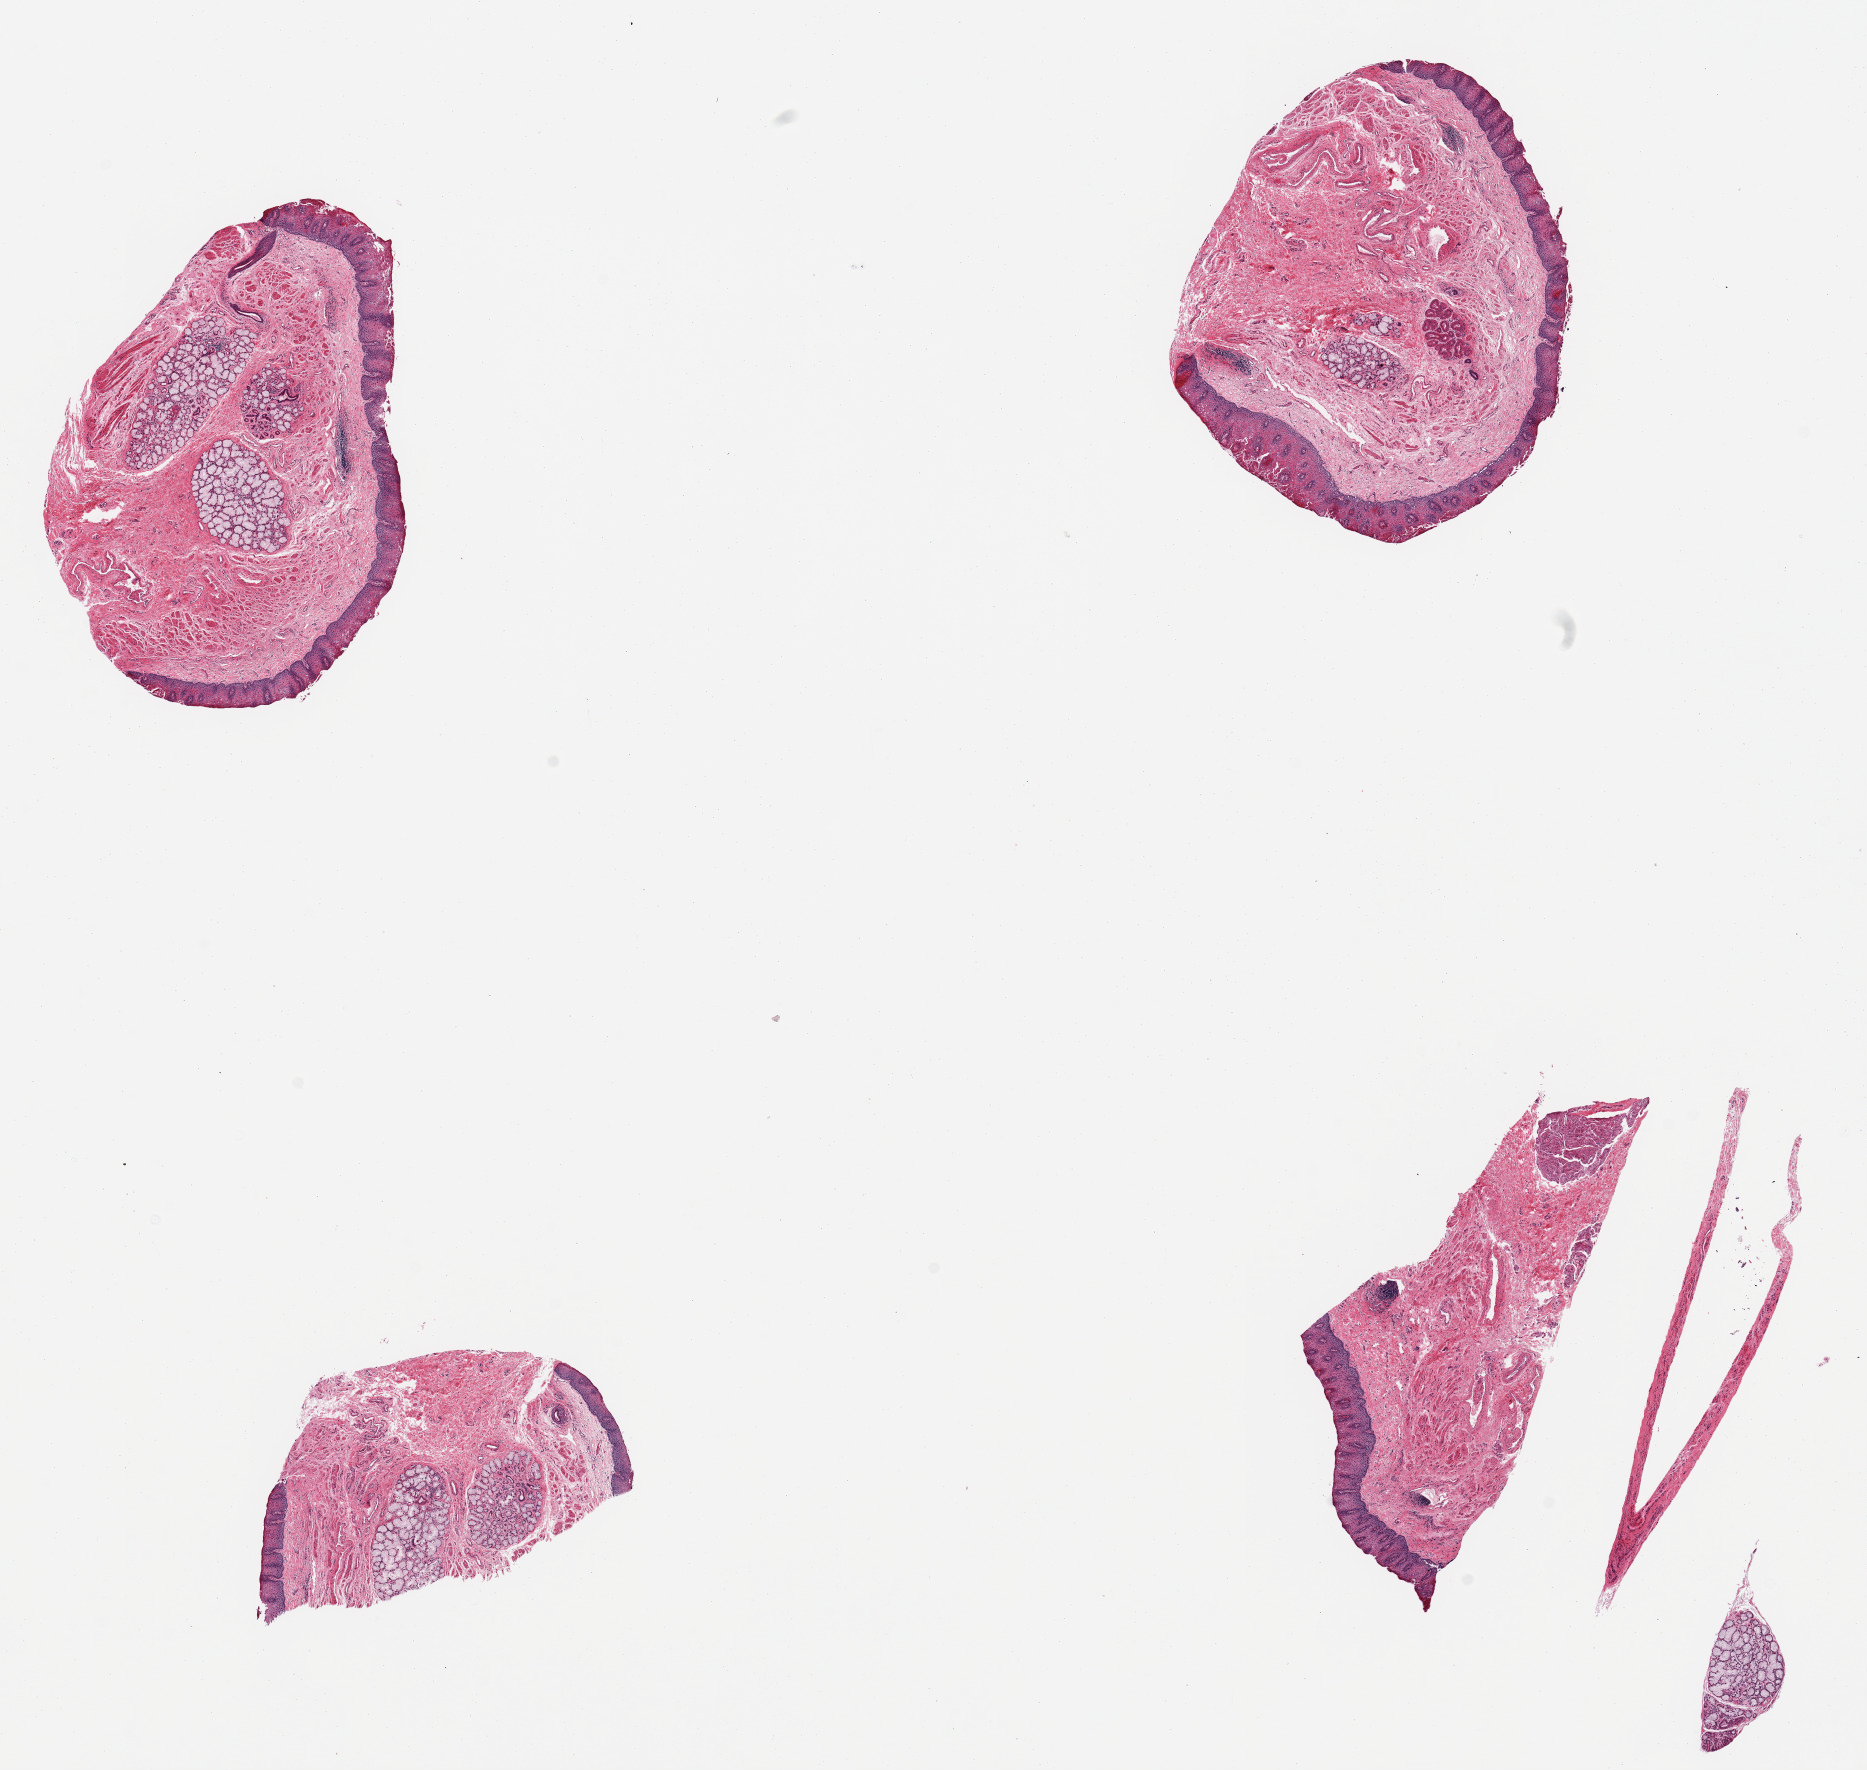
Whole-slide image, haematoxylin and eosin stain, shown as a low-resolution overview of the whole scanned area (about 14.8 x 14.0 mm); PAXgene-fixed paraffin-embedded (PFPE) section; section of esophageal mucous membrane (target tissue); tissue donor sample. Donor: male.
Review note (as recorded): 4 pieces; squamous epithelim up to 224.4um thick; submucosal mucus glands occupy up to 20%.